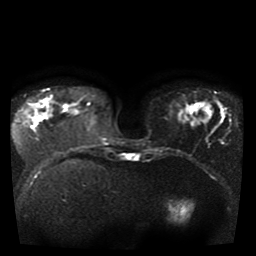
Breast MRI, one axial slice. Position 12 of 41 along the scan axis. Diffusion-weighted series; image 2 of 4 stored at this slice position (different b-values; order by instance number). 1.5 T. 5 mm slice thickness. 256 × 256 image matrix, field of view 330 × 330 mm. Female patient.
Outlined on this slice (manually delineated by an expert):
- tumour on diffusion-weighted imaging: box from (x=31, y=103) to (x=46, y=122) px